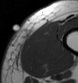
MRI of an extremity soft-tissue mass, one axial slice; MR volume resampled by the dataset authors to the PET/CT grid (not the native acquisition matrix); 3.27 mm slice thickness; 78 × 83 image matrix, field of view 76 × 81 mm. Male patient. Case-level facts recorded for this patient, not image findings: histological type: pleiomorphic leiomyosarcoma; grade: high; site of the primary tumour: left thigh.
Outlined on this slice (expert contour drawn on MRI and transferred to this co-registered scan by the dataset authors):
- gross tumour volume including surrounding oedema: bounding box [x1, y1, x2, y2] px = [24, 21, 58, 73]